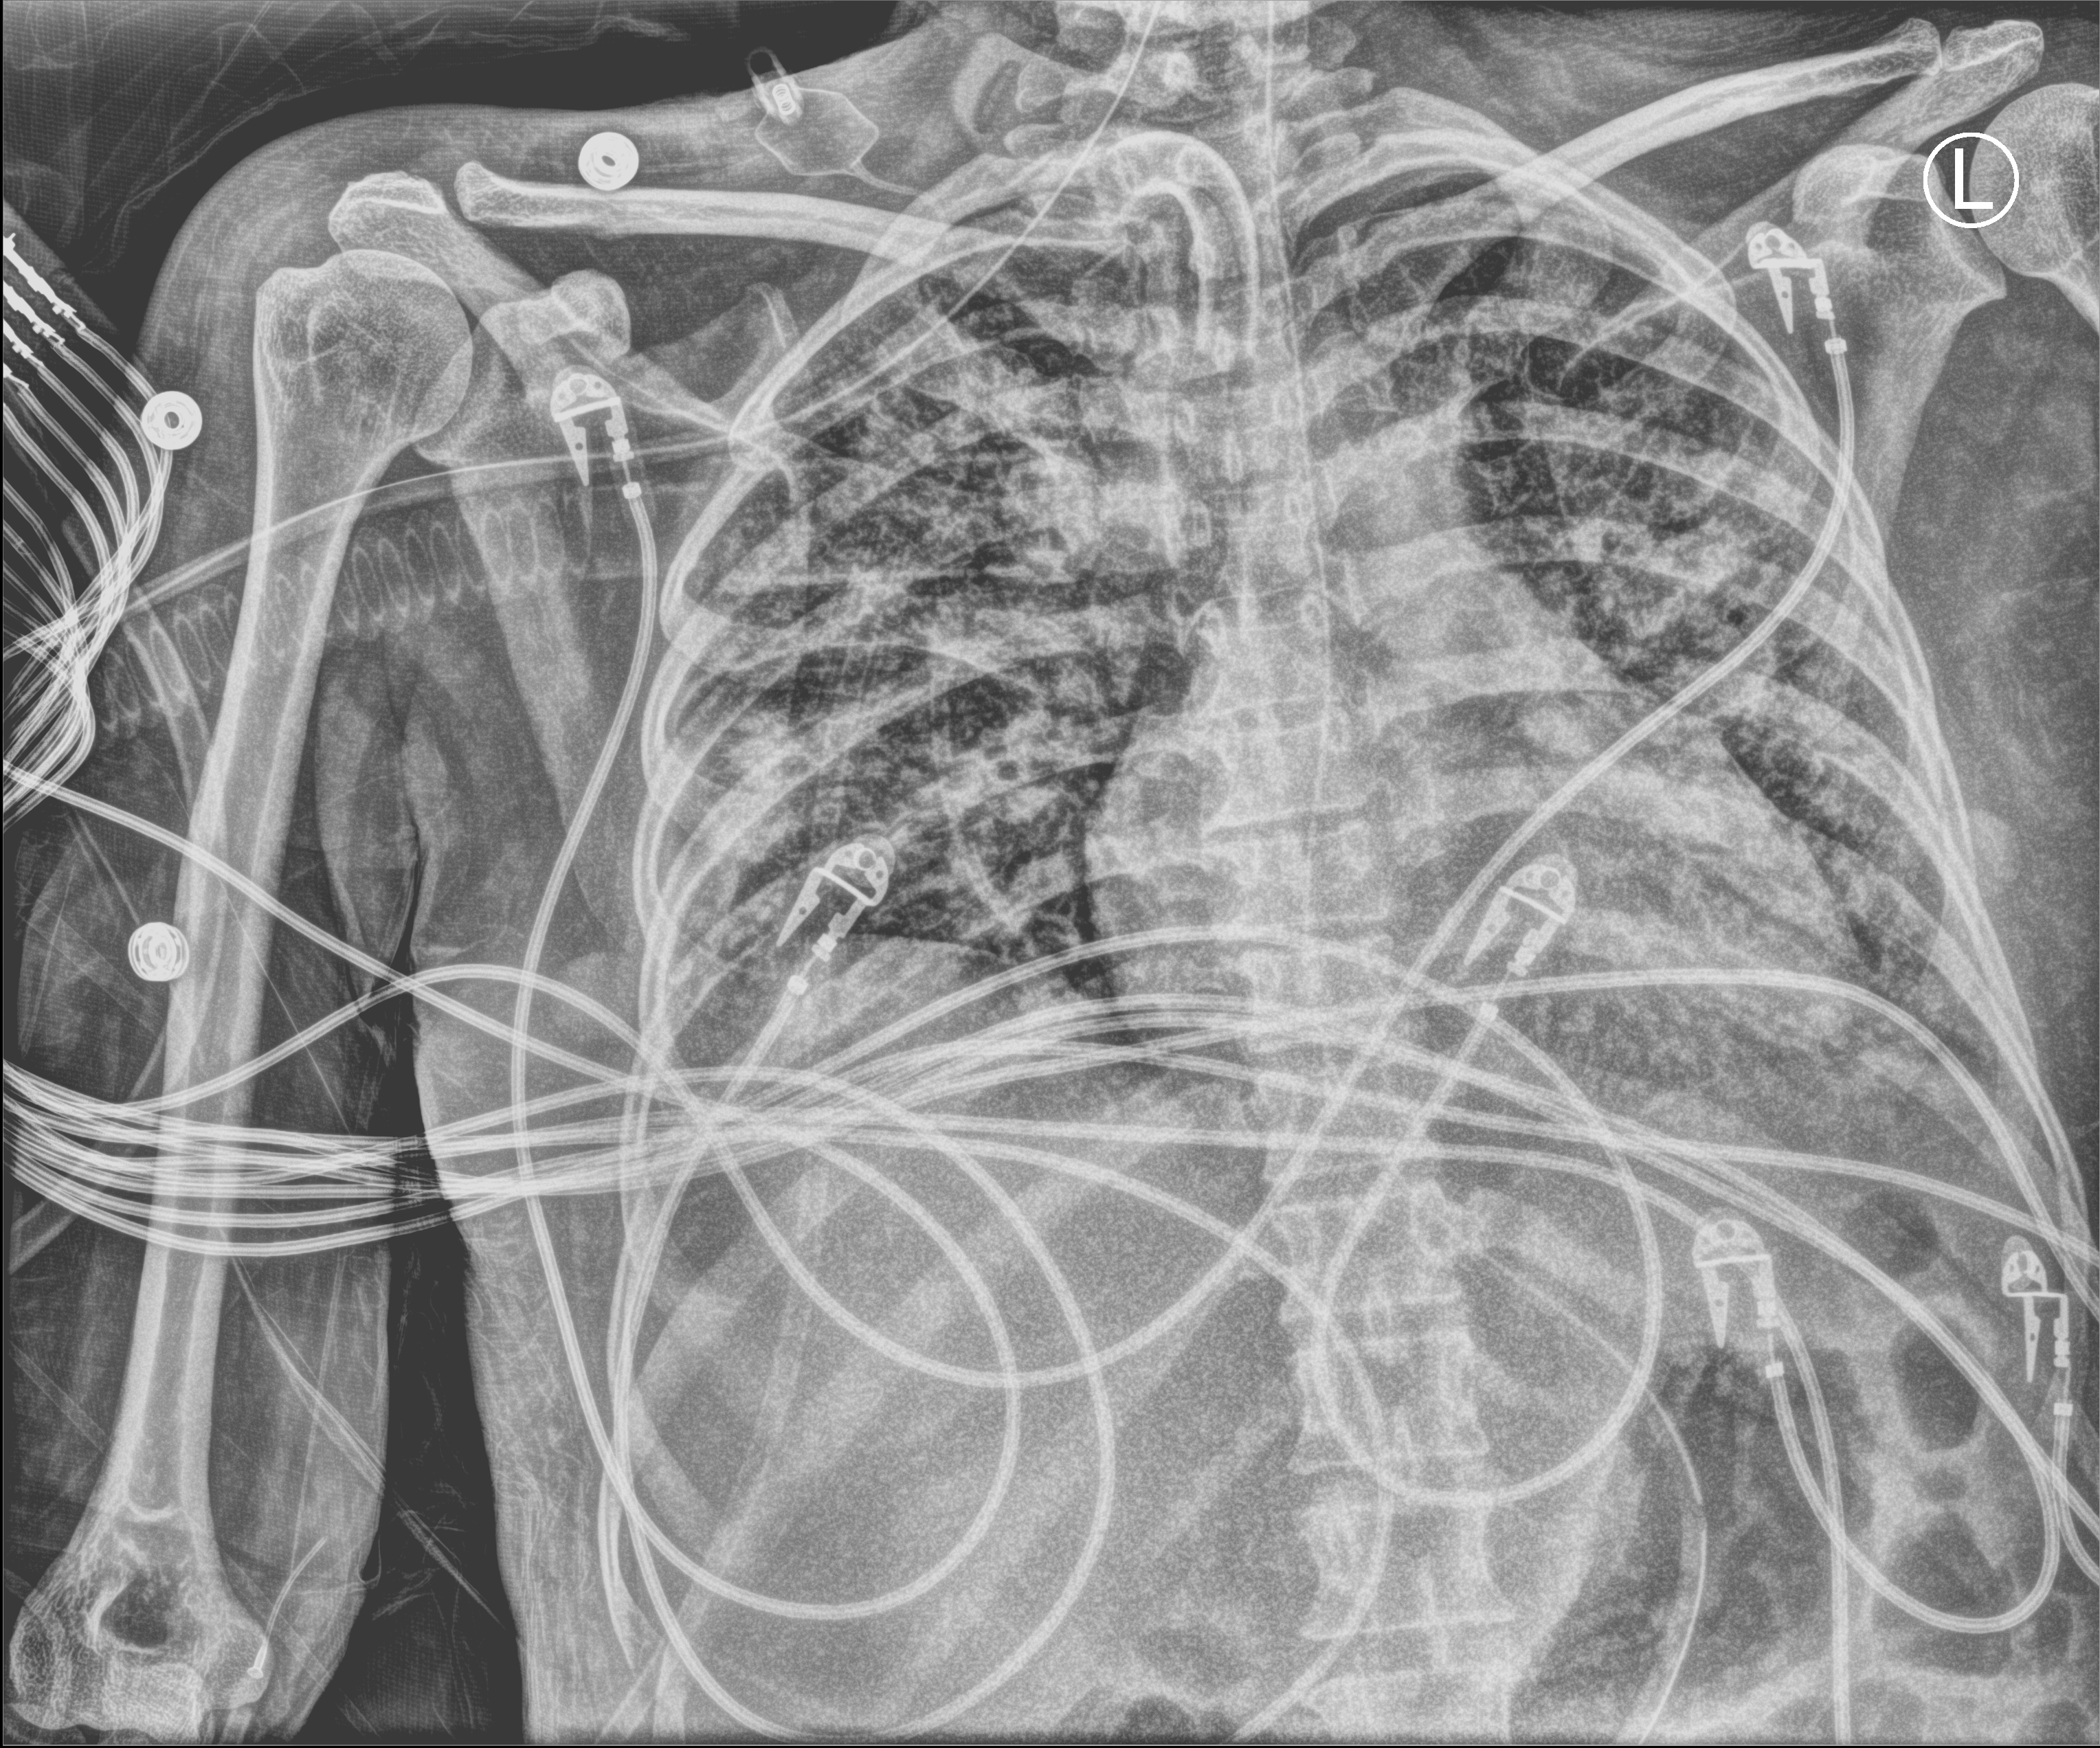
Bedside chest radiograph (computed radiography), anteroposterior (AP) projection. Patient hospitalised with COVID-19; female, aged 18–59 years.
Admission-level facts for this patient (not findings on this image; timing relative to this image not recorded): length of hospital stay: 71 days.